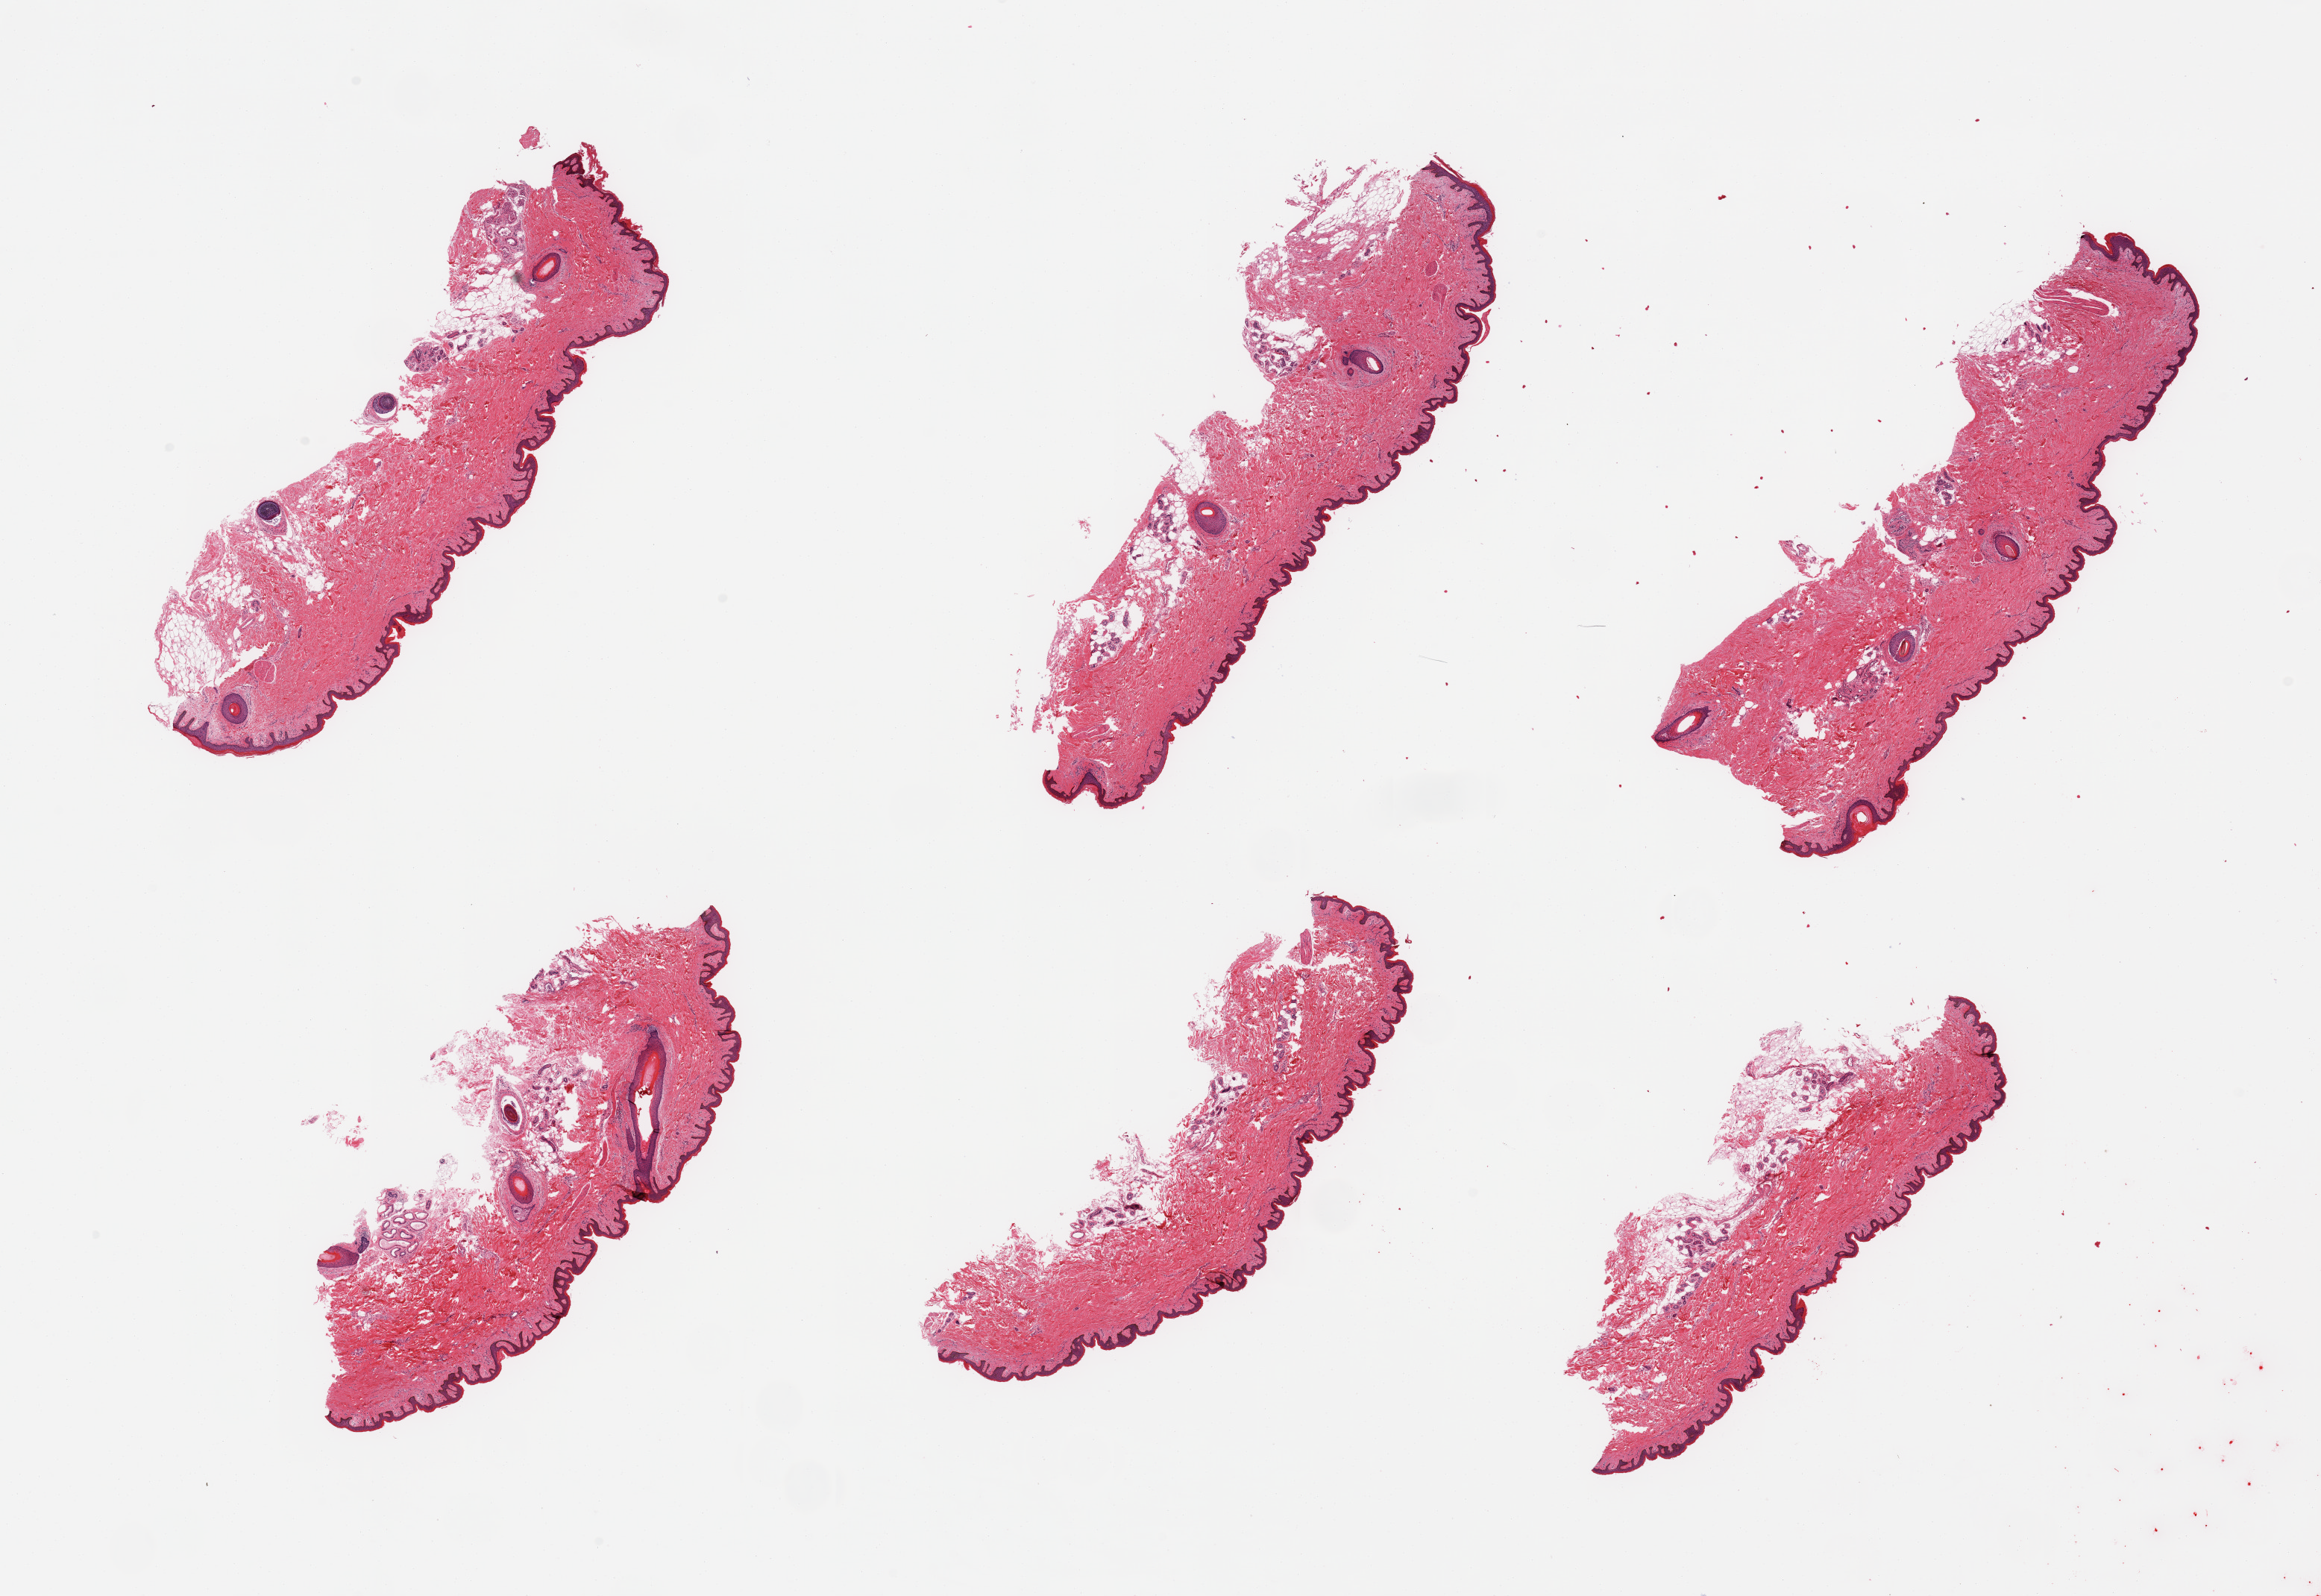
Whole-slide image, hematoxylin and eosin (H&E) stain — low-resolution overview of the scanned area, about 24.6 x 16.9 mm (from a 20x scan). PAXgene-fixed paraffin-embedded (PFPE) section. Section of skin of suprapubic region (target tissue). Tissue donor sample. Female donor.
Review note (as recorded): 6 pieces; well trimmed; 10% dermall fat.